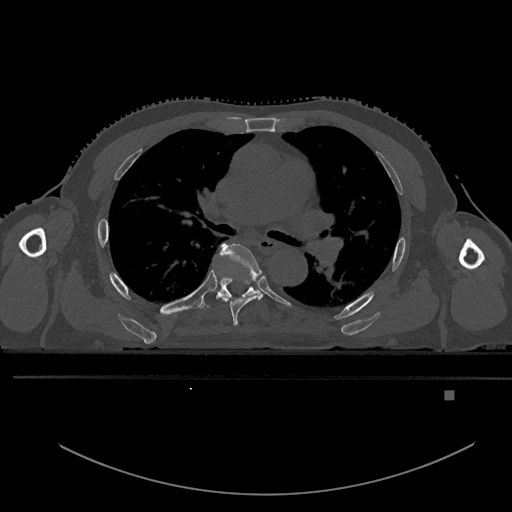
CT including the spine, one axial slice. Slice 336 of 969 in the series (ordered by position). Bone window (W 1800 / L 400 HU). 0.5 mm slice thickness. 512 × 512 image matrix. Male patient, age 82 years. From the clinical record (not read from this slice): primary cancer: prostate.
Structures marked on this image (semi-automatic segmentation, software-assisted and operator-edited):
- T5 vertebra: box from (x=214, y=243) to (x=263, y=327) px
- T6 vertebra: (x=198, y=277)–(x=260, y=310)